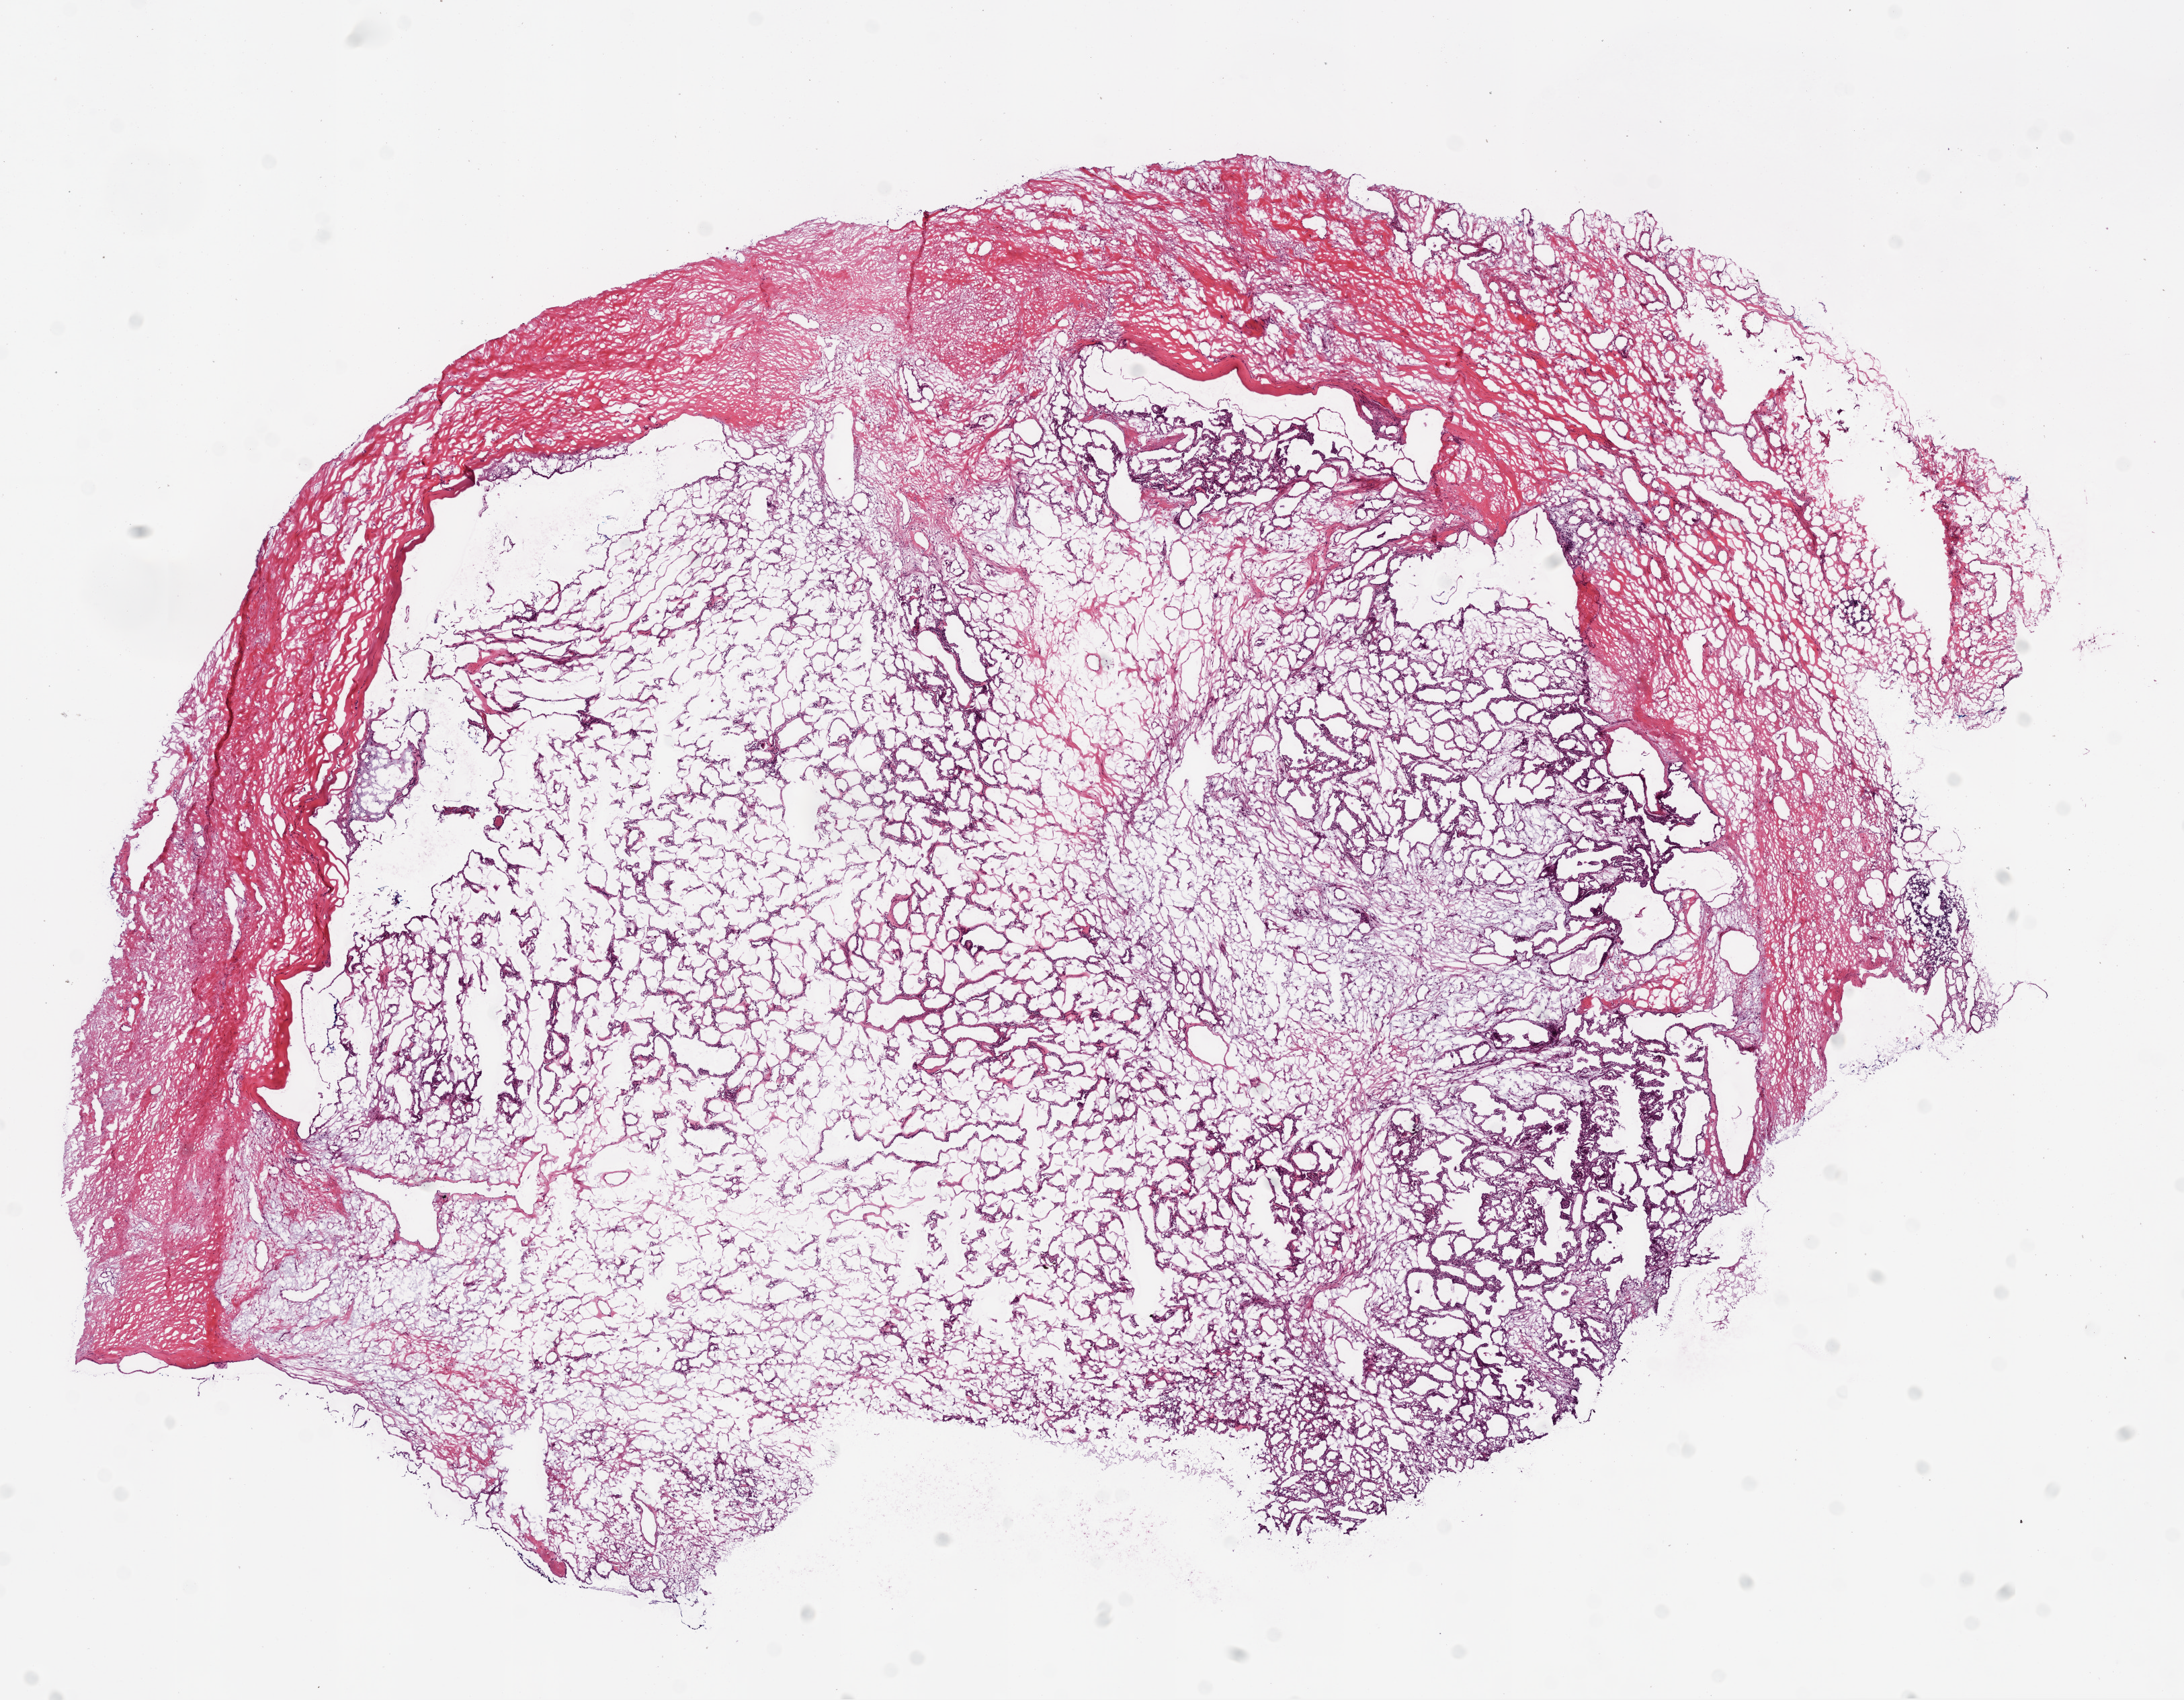
Whole-slide histology image, H&E, shown as a low-resolution overview of the whole scanned area (about 13.0 x 10.2 mm); frozen section from the bottom of the tissue portion; kidney, primary tumour sample. Female, age 67 years at initial diagnosis.
Histologic diagnosis: Clear cell adenocarcinoma, NOS.